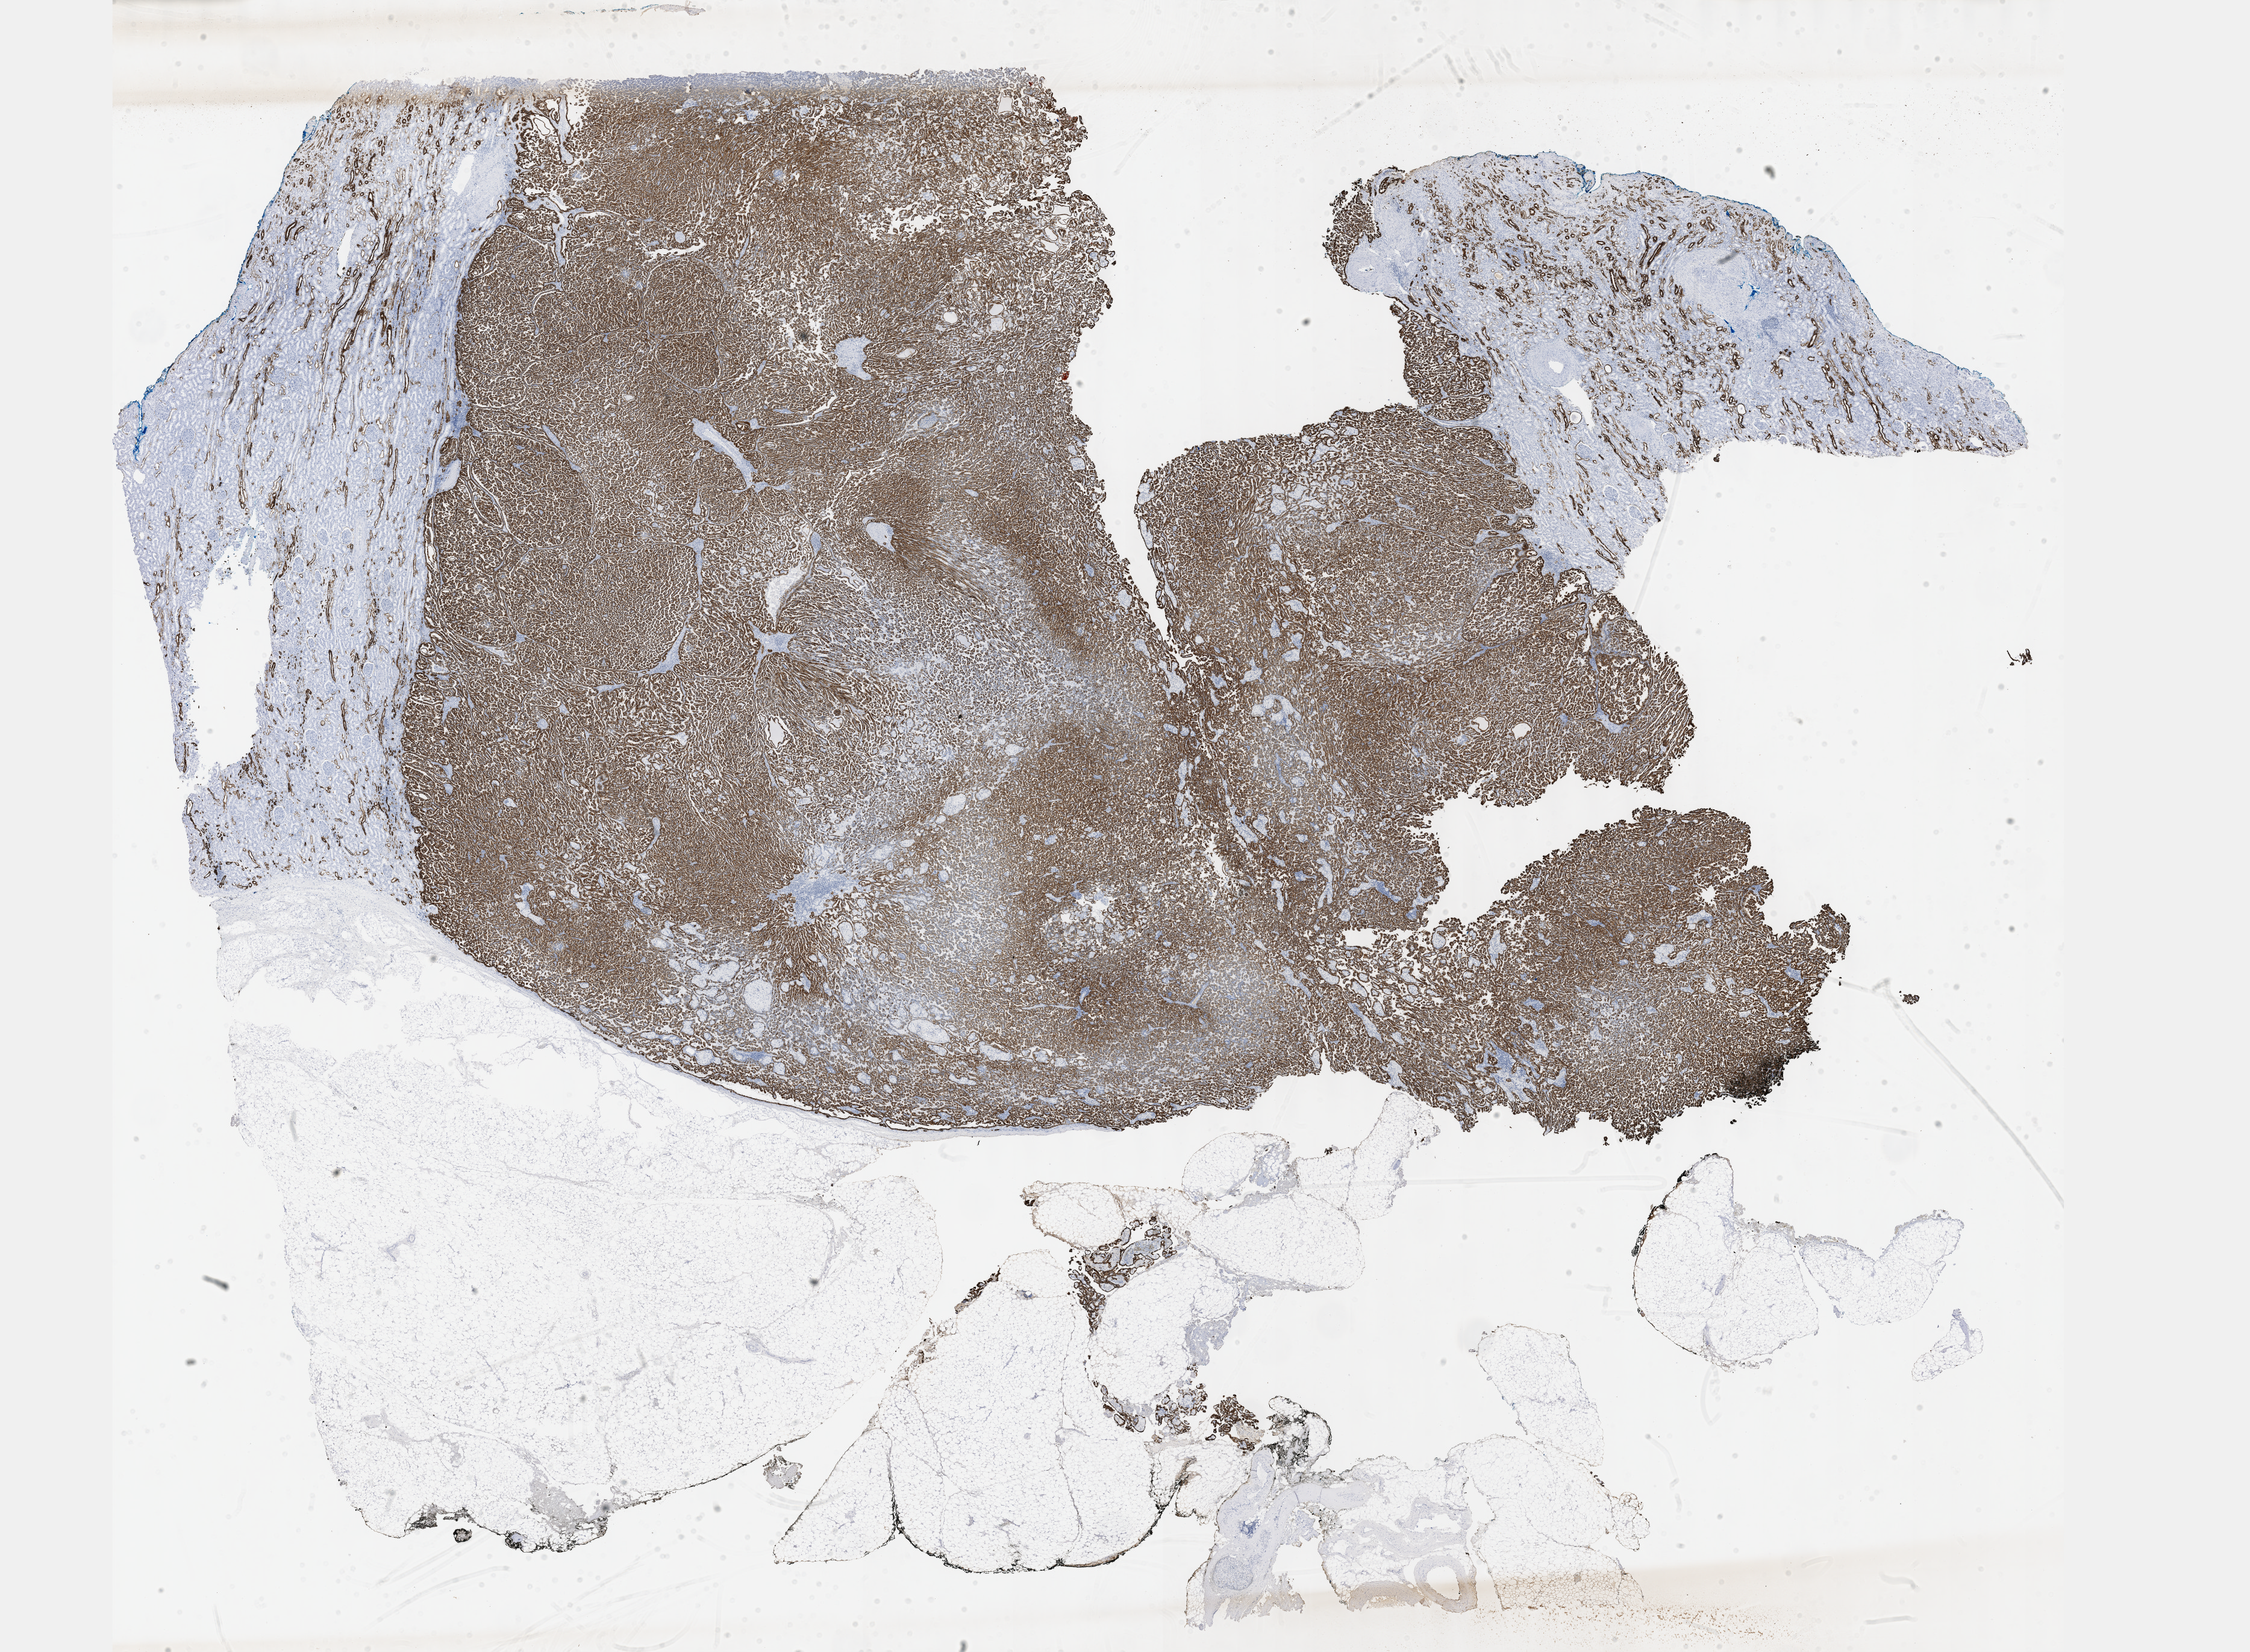
Digitized H&E-stained tissue section (whole slide) — low-resolution overview of the scanned area, about 30.2 x 22.2 mm (slide scanned at 40x), formalin-fixed paraffin-embedded (FFPE) diagnostic section, sample: primary tumour, kidney. Male, age 65 years at initial diagnosis.
Histologic diagnosis: Papillary adenocarcinoma, NOS.